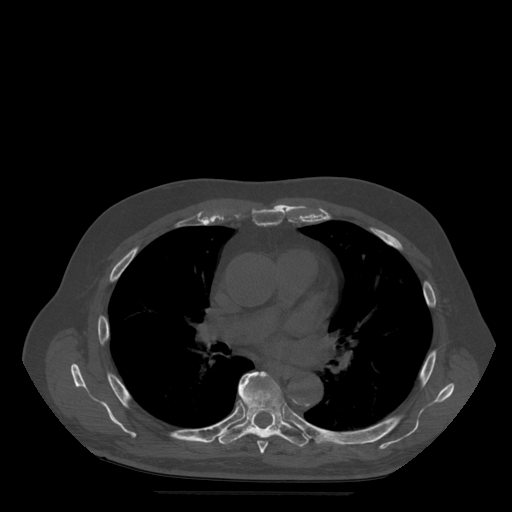
CT including the spine, one axial slice; slice 340 of 522 in the series (ordered by position); bone window (W 1800 / L 400 HU); 1.25 mm slice thickness; 512 × 512 image matrix, field of view 420 × 420 mm. Patient age 72 years. Case-level facts recorded for this patient, not image findings: primary cancer: prostate.
Outlined on this slice (semi-automatic segmentation, software-assisted and operator-edited):
- T6 vertebra: bounding box (x1, y1, x2, y2) in pixels: (239, 372, 275, 454)
- T7 vertebra: (216, 374, 310, 447)